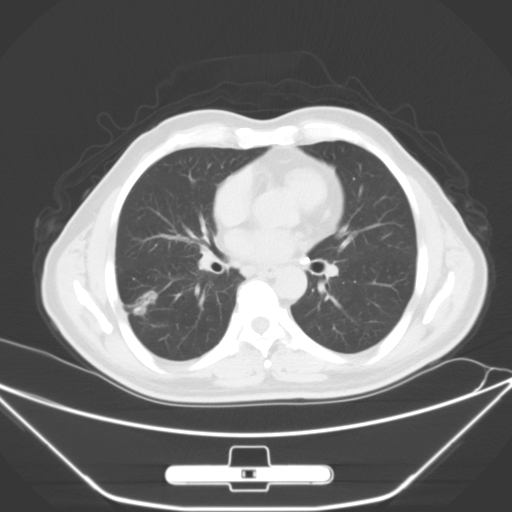
Chest CT, one axial slice; slice 29 of 62 in the series (ordered by position); lung window (W 1500 / L -600 HU); 512 × 512 image matrix, field of view 398 × 398 mm. Male patient, age 71 years. Case-level facts recorded for this patient, not image findings: clinical TNM (as recorded): T1c N0 M0; histopathological grade: G2.
Annotated regions visible in this slice (rectangle marked by the reading radiologist):
- lung tumour (recorded histology: adenocarcinoma): bounding box (x1, y1, x2, y2) in pixels: (128, 286, 166, 318)